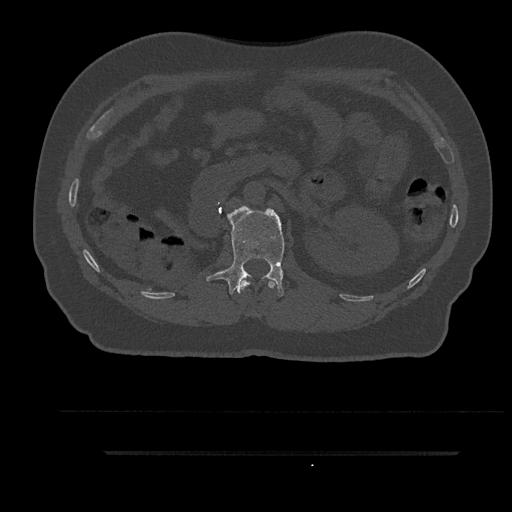
CT including the spine, one axial slice. Slice 184 of 797 in the series (ordered by position). 120 kVp. Bone window (W 1800 / L 400 HU). 0.5 mm slice thickness. 512 × 512 image matrix. Male patient, age 63 years. From the clinical record (not read from this slice): primary cancer: renal; vertebrae with lytic lesions (as recorded): T8.
Annotated regions visible in this slice (semi-automatic segmentation, software-assisted and operator-edited):
- L1 vertebra: box from (x=206, y=207) to (x=285, y=297) px
- T12 vertebra: (x=240, y=280)–(x=277, y=291)